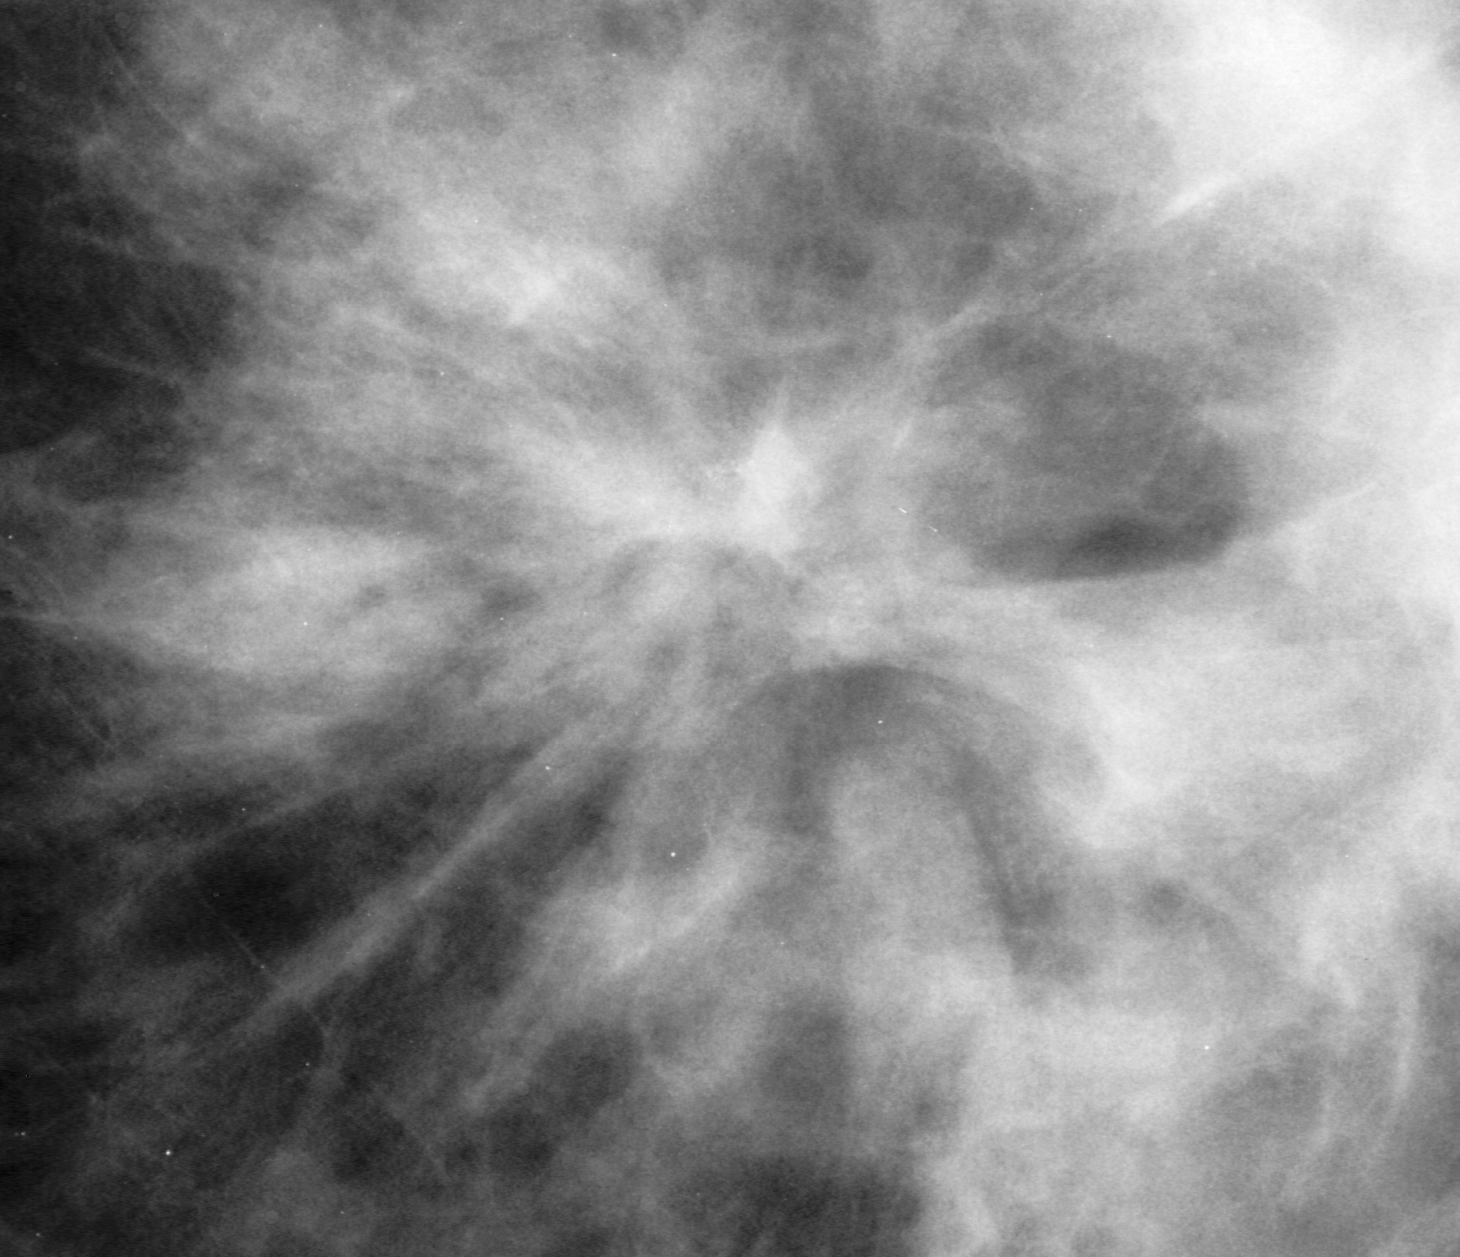
Crop from a digitized film mammogram around one marked abnormality; right breast; CC view.
Calcifications, morphology pleomorphic, distribution clustered; BI-RADS assessment category 5; subtlety rating 4 on a 1 (subtle) to 5 (obvious) scale; pathology (as recorded): malignant.